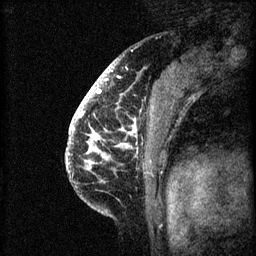
Breast MRI (dynamic contrast-enhanced), one sagittal slice. Position 45 of 60 along the scan axis. 3 images stored at this slice position (order not interpretable as contrast timing). 1.5 T. TE 4.2 ms, TR 8.2 ms. 256 × 256 image matrix, field of view 180 × 180 mm. Patient: female, 41 years.
Structures marked on this image (semi-automatically segmented with operator editing):
- analysis volume of interest (the breast-tissue region the enhancement analysis was run in; not a lesion): bounding box [x1, y1, x2, y2] px = [72, 108, 156, 205]
- tumour enhancement mask (voxels above the 70 % enhancement threshold inside the analysis volume of interest): [72, 108, 137, 165]